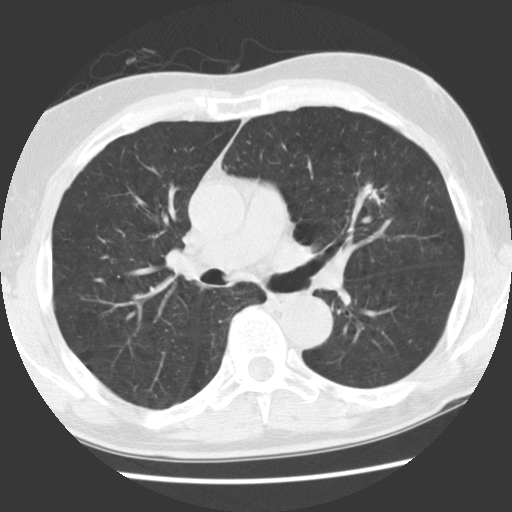
Low-dose screening chest CT, axial slice; first (baseline) screen; lung window (W 1500 / L -600 HU); 2.5 mm slice thickness; standard (soft-tissue) reconstruction kernel (STANDARD); slice 77 of 131 in the series. Male participant, aged 70 years at enrolment. Current smoker at enrolment.
Expert-annotated lung lesion, bounding box <342,172,399,221> (left, top, right, bottom; pixels). The screening reader recorded 2 non-calcified nodules or masses ≥4 mm on this exam (left upper lobe, right lower lobe); which of them this box marks is not recorded. Later outcome: lung cancer diagnosed 879 days after this screen (after the third annual screen) — adenocarcinoma, NOS, left upper lobe, moderately differentiated (G2), stage IIIA (AJCC 6th edition), 17 mm at pathology.